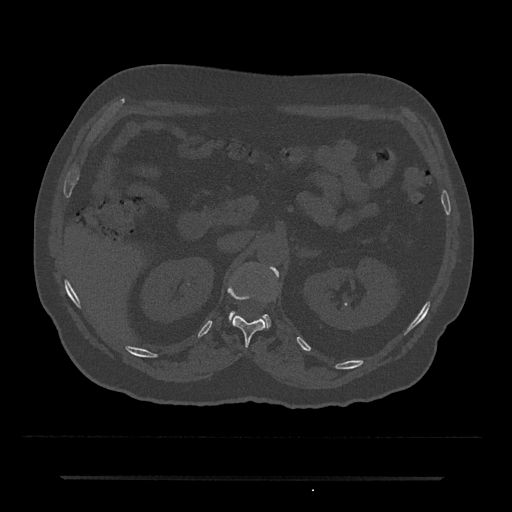
CT including the spine, one axial slice. Slice 111 of 797 in the series (ordered by position). Reconstruction kernel Br40s/3. Bone window (W 1800 / L 400 HU). 0.5 mm slice thickness. 512 × 512 image matrix, field of view 437 × 437 mm. Male patient, age 69 years. From the clinical record (not read from this slice): primary cancer: prostate.
Annotated regions visible in this slice (semi-automatic segmentation, software-assisted and operator-edited):
- L1 vertebra: bounding box [x1, y1, x2, y2] px = [229, 266, 279, 327]
- T12 vertebra: [227, 284, 267, 347]